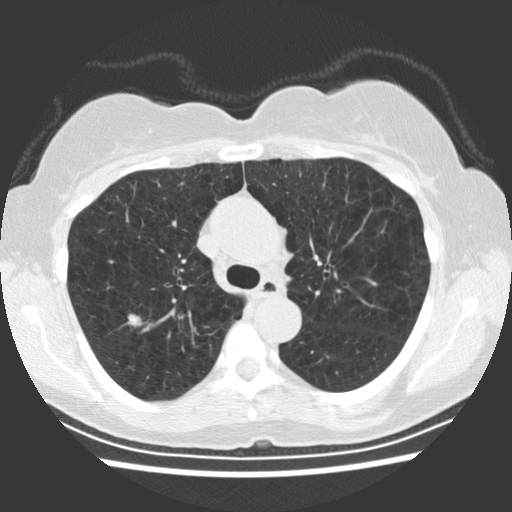
Low-dose screening chest CT, one axial slice; position 165 of 234 along the scan axis; reconstruction kernel STANDARD; 120 kVp; lung window (W 1500 / L -600 HU); 2.5 mm slice thickness; 512 × 512 image matrix, field of view 330 × 330 mm.
Outlined on this slice (manually delineated by an expert):
- lesion 1 (tumor, upper lobe of right lung): box from (x=127, y=314) to (x=143, y=327) px